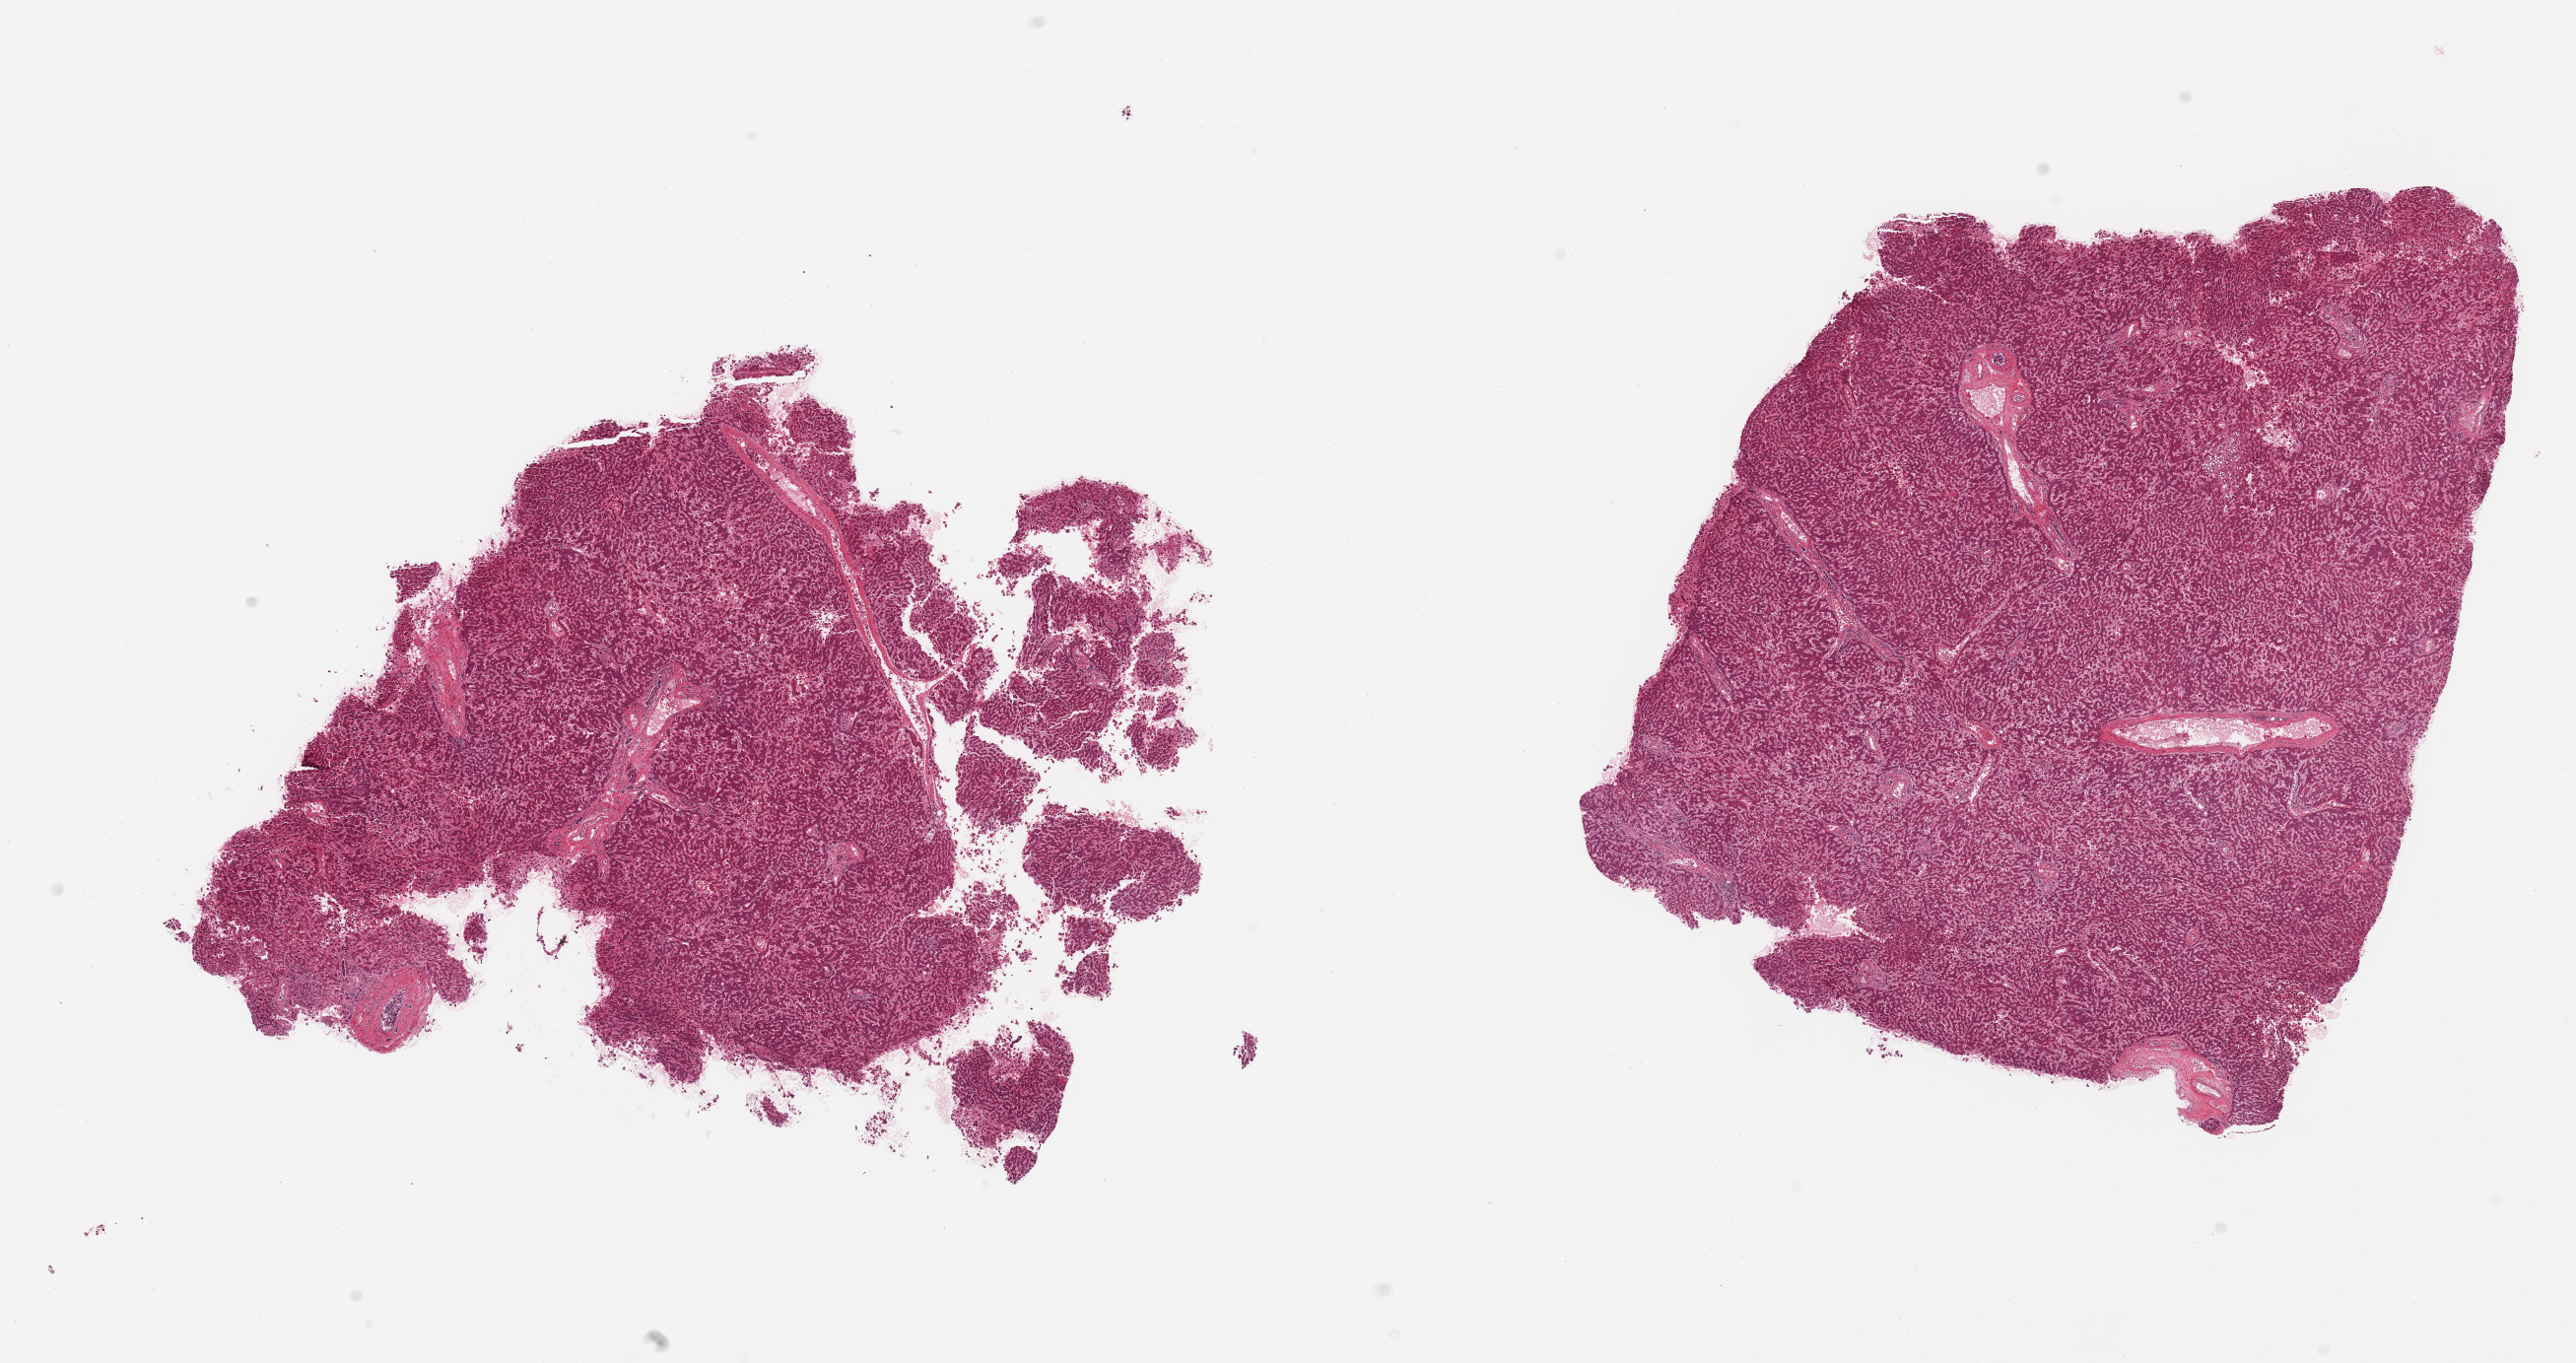
Whole-slide image, hematoxylin and eosin (H&E) stain — whole scanned area (about 20.7 x 10.9 mm, from a 20x scan) shown as a low-resolution overview; PAXgene-fixed paraffin-embedded (PFPE) section; section of liver (target tissue); donor tissue sample. Donor: female.
* reviewer comment on this tissue sample: 2 pieces, moderate congestions; macrovesicular steatosis in ~20% of parenchyma